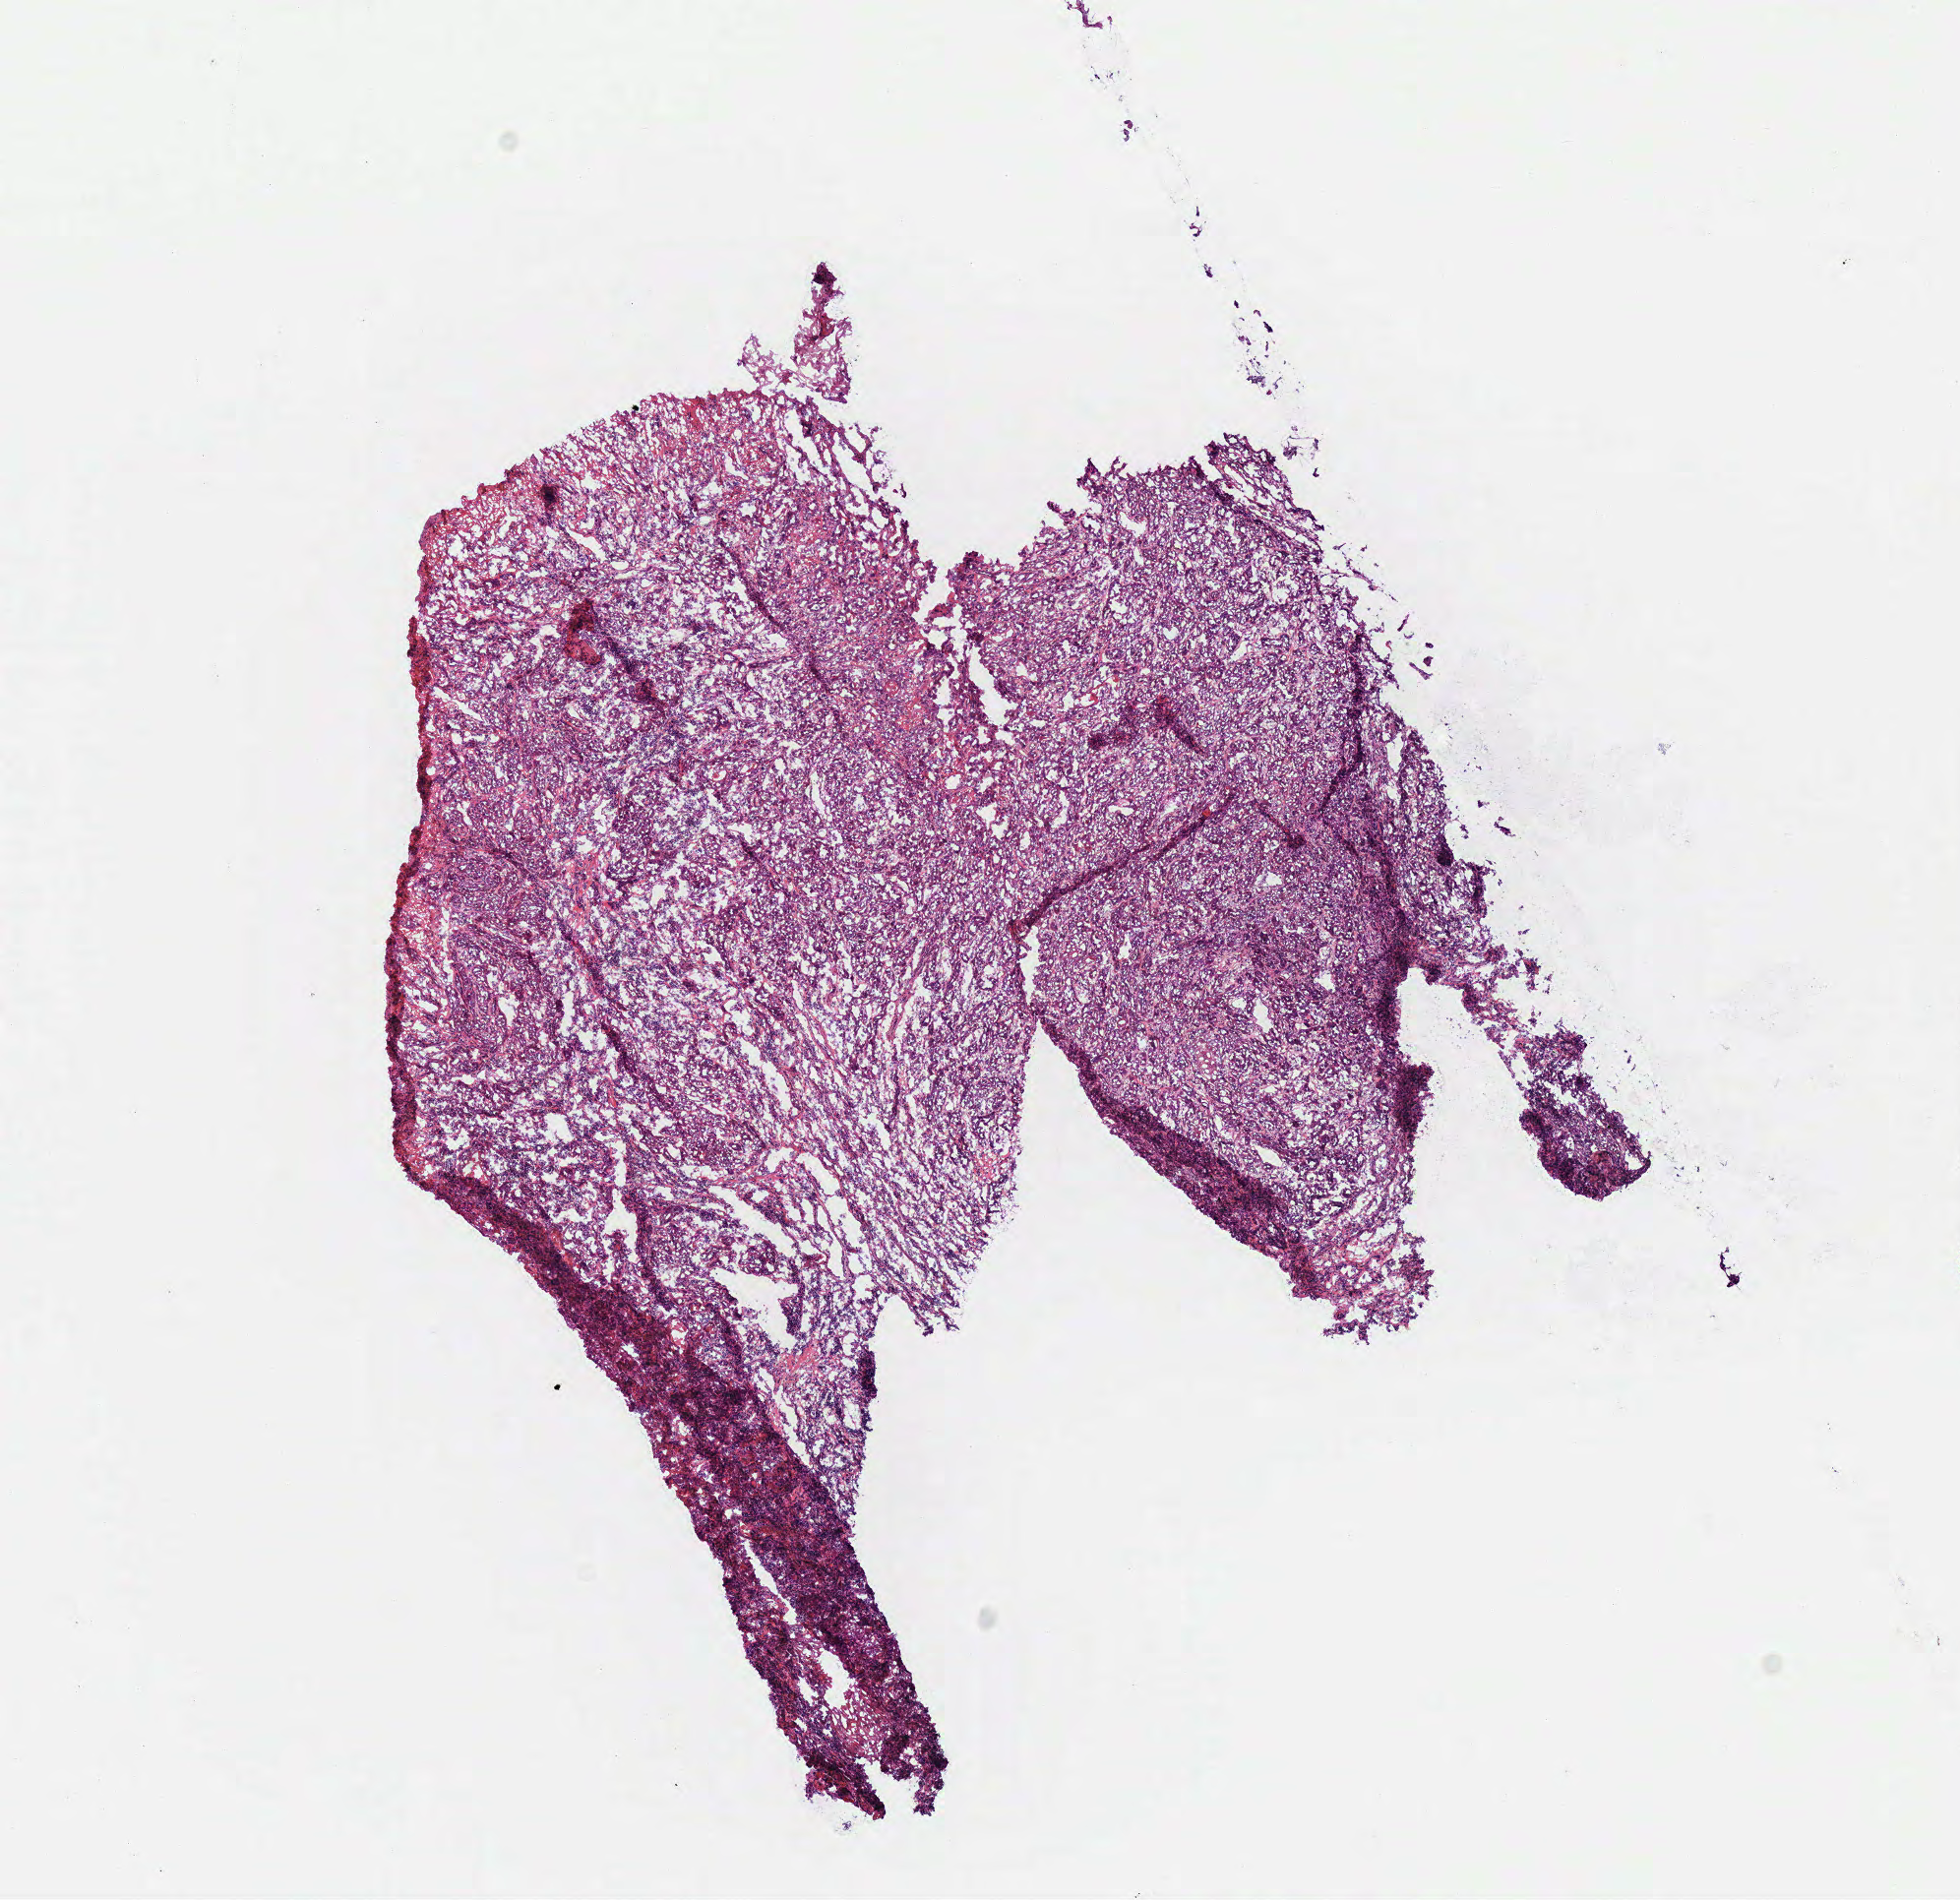
Digitized H&E-stained tissue section (whole slide), a low-resolution overview of the entire scanned area, about 7.8 x 7.6 mm (acquisition: 40x scan); frozen section; head and neck, primary tumour sample. Patient: male, age at initial diagnosis 74 years. Histologic grade: G2 (moderately differentiated). Slide review estimates, as recorded: tumour cells 90%, tumour nuclei 65%, normal cells 0%, stromal cells 10%, necrosis 0%.
• AJCC pathologic stage: IVA (7th edition)
• pathologic diagnosis: Squamous cell carcinoma, NOS (larynx, NOS)